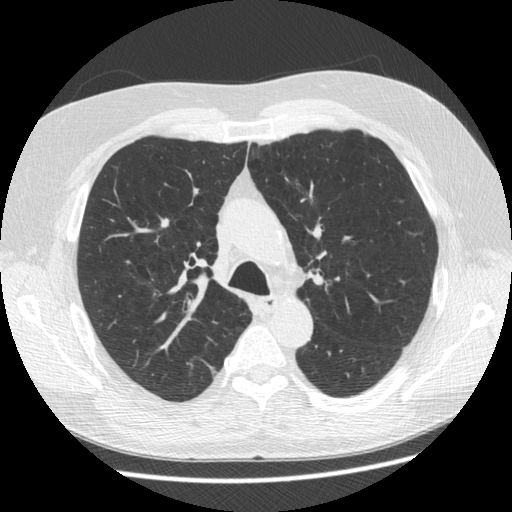
Chest CT (low-dose screening protocol), one axial image; third screening round (two years after baseline); lung window (W 1500 / L -600 HU); standard (soft-tissue) reconstruction kernel (STANDARD); 120 kVp; 512 × 512 image matrix, field of view 360 × 360 mm. Male, age 63 years at enrolment. Former smoker at enrolment.
• Expert-annotated lung lesion, bounding box (x1, y1, x2, y2) in pixels: (150, 209, 182, 238).
• The screening reader recorded 2 non-calcified nodules or masses ≥4 mm on this exam (right upper lobe, left upper lobe); which of them this box marks is not recorded.
• Official screen result: positive, other.